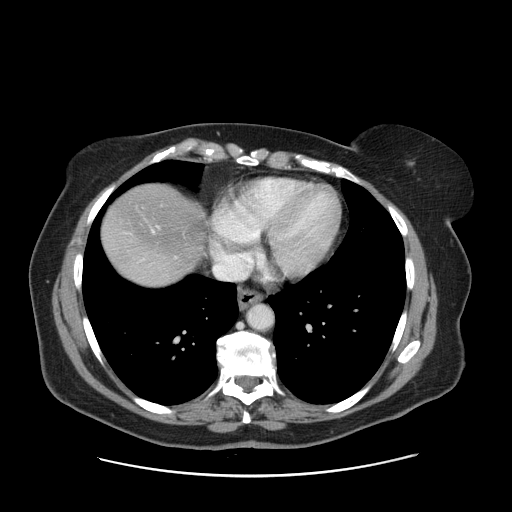
Contrast-enhanced abdominal CT, one axial slice; position 145 of 161 along the scan axis; 120 kVp; soft-tissue window (W 400 / L 40 HU); 2.5 mm slice thickness; 512 × 512 image matrix, field of view 398 × 398 mm. Female patient, age 62 years. Case-level facts recorded for this patient, not image findings: diagnosis: colorectal cancer liver metastases, imaged before liver resection; multiple liver metastases: no; largest metastasis: 2.5 cm; disease in both lobes: no.
Structures marked on this image (manually delineated by an expert):
- hepatic veins: bounding box [x1, y1, x2, y2] px = [152, 229, 155, 233]
- liver: [102, 185, 205, 285]
- planned liver remnant (the part of the liver to remain after resection): [104, 185, 204, 270]